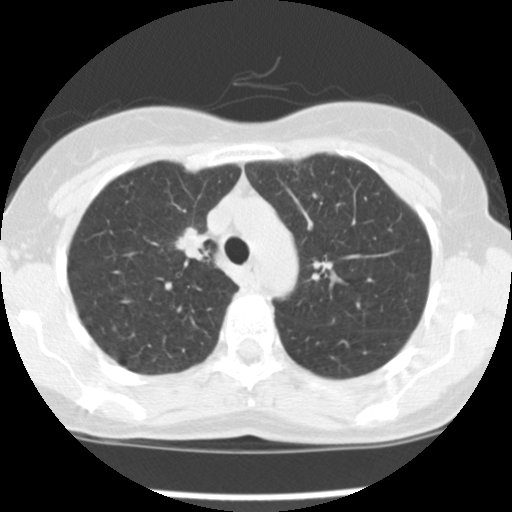
Low-dose screening chest CT, one axial slice. Position 115 of 157 along the scan axis. Reconstruction kernel STANDARD. Lung window (W 1500 / L -600 HU). 512 × 512 image matrix, field of view 282 × 282 mm.
Outlined on this slice (outlined manually by an expert reader):
- lesion 1 (tumor, upper lobe of right lung): box from (x=175, y=227) to (x=207, y=259) px